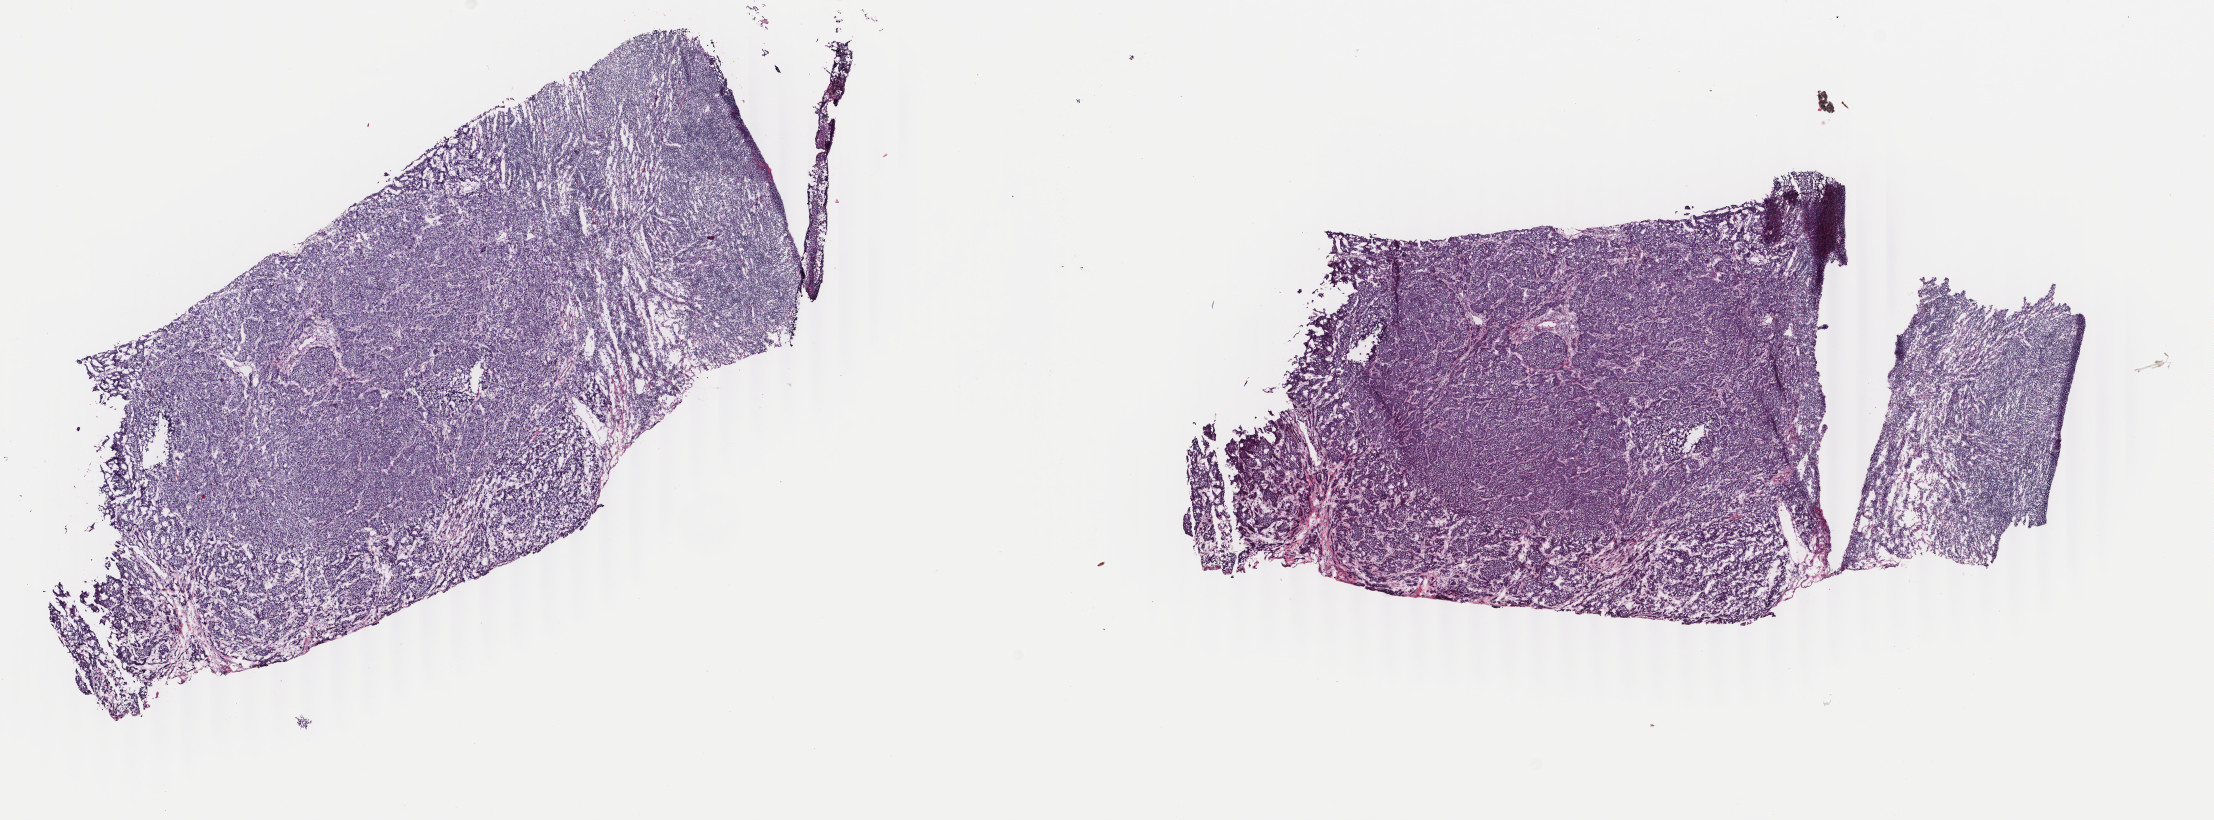
Whole-slide histology image, H&E — low-resolution overview of the scanned area, about 17.6 x 6.5 mm (acquisition: 40x scan); frozen section from the top of the tissue portion; sample: primary tumour, breast. Patient: female, age at initial diagnosis 68 years.
Pathologic diagnosis: Infiltrating duct carcinoma, NOS.